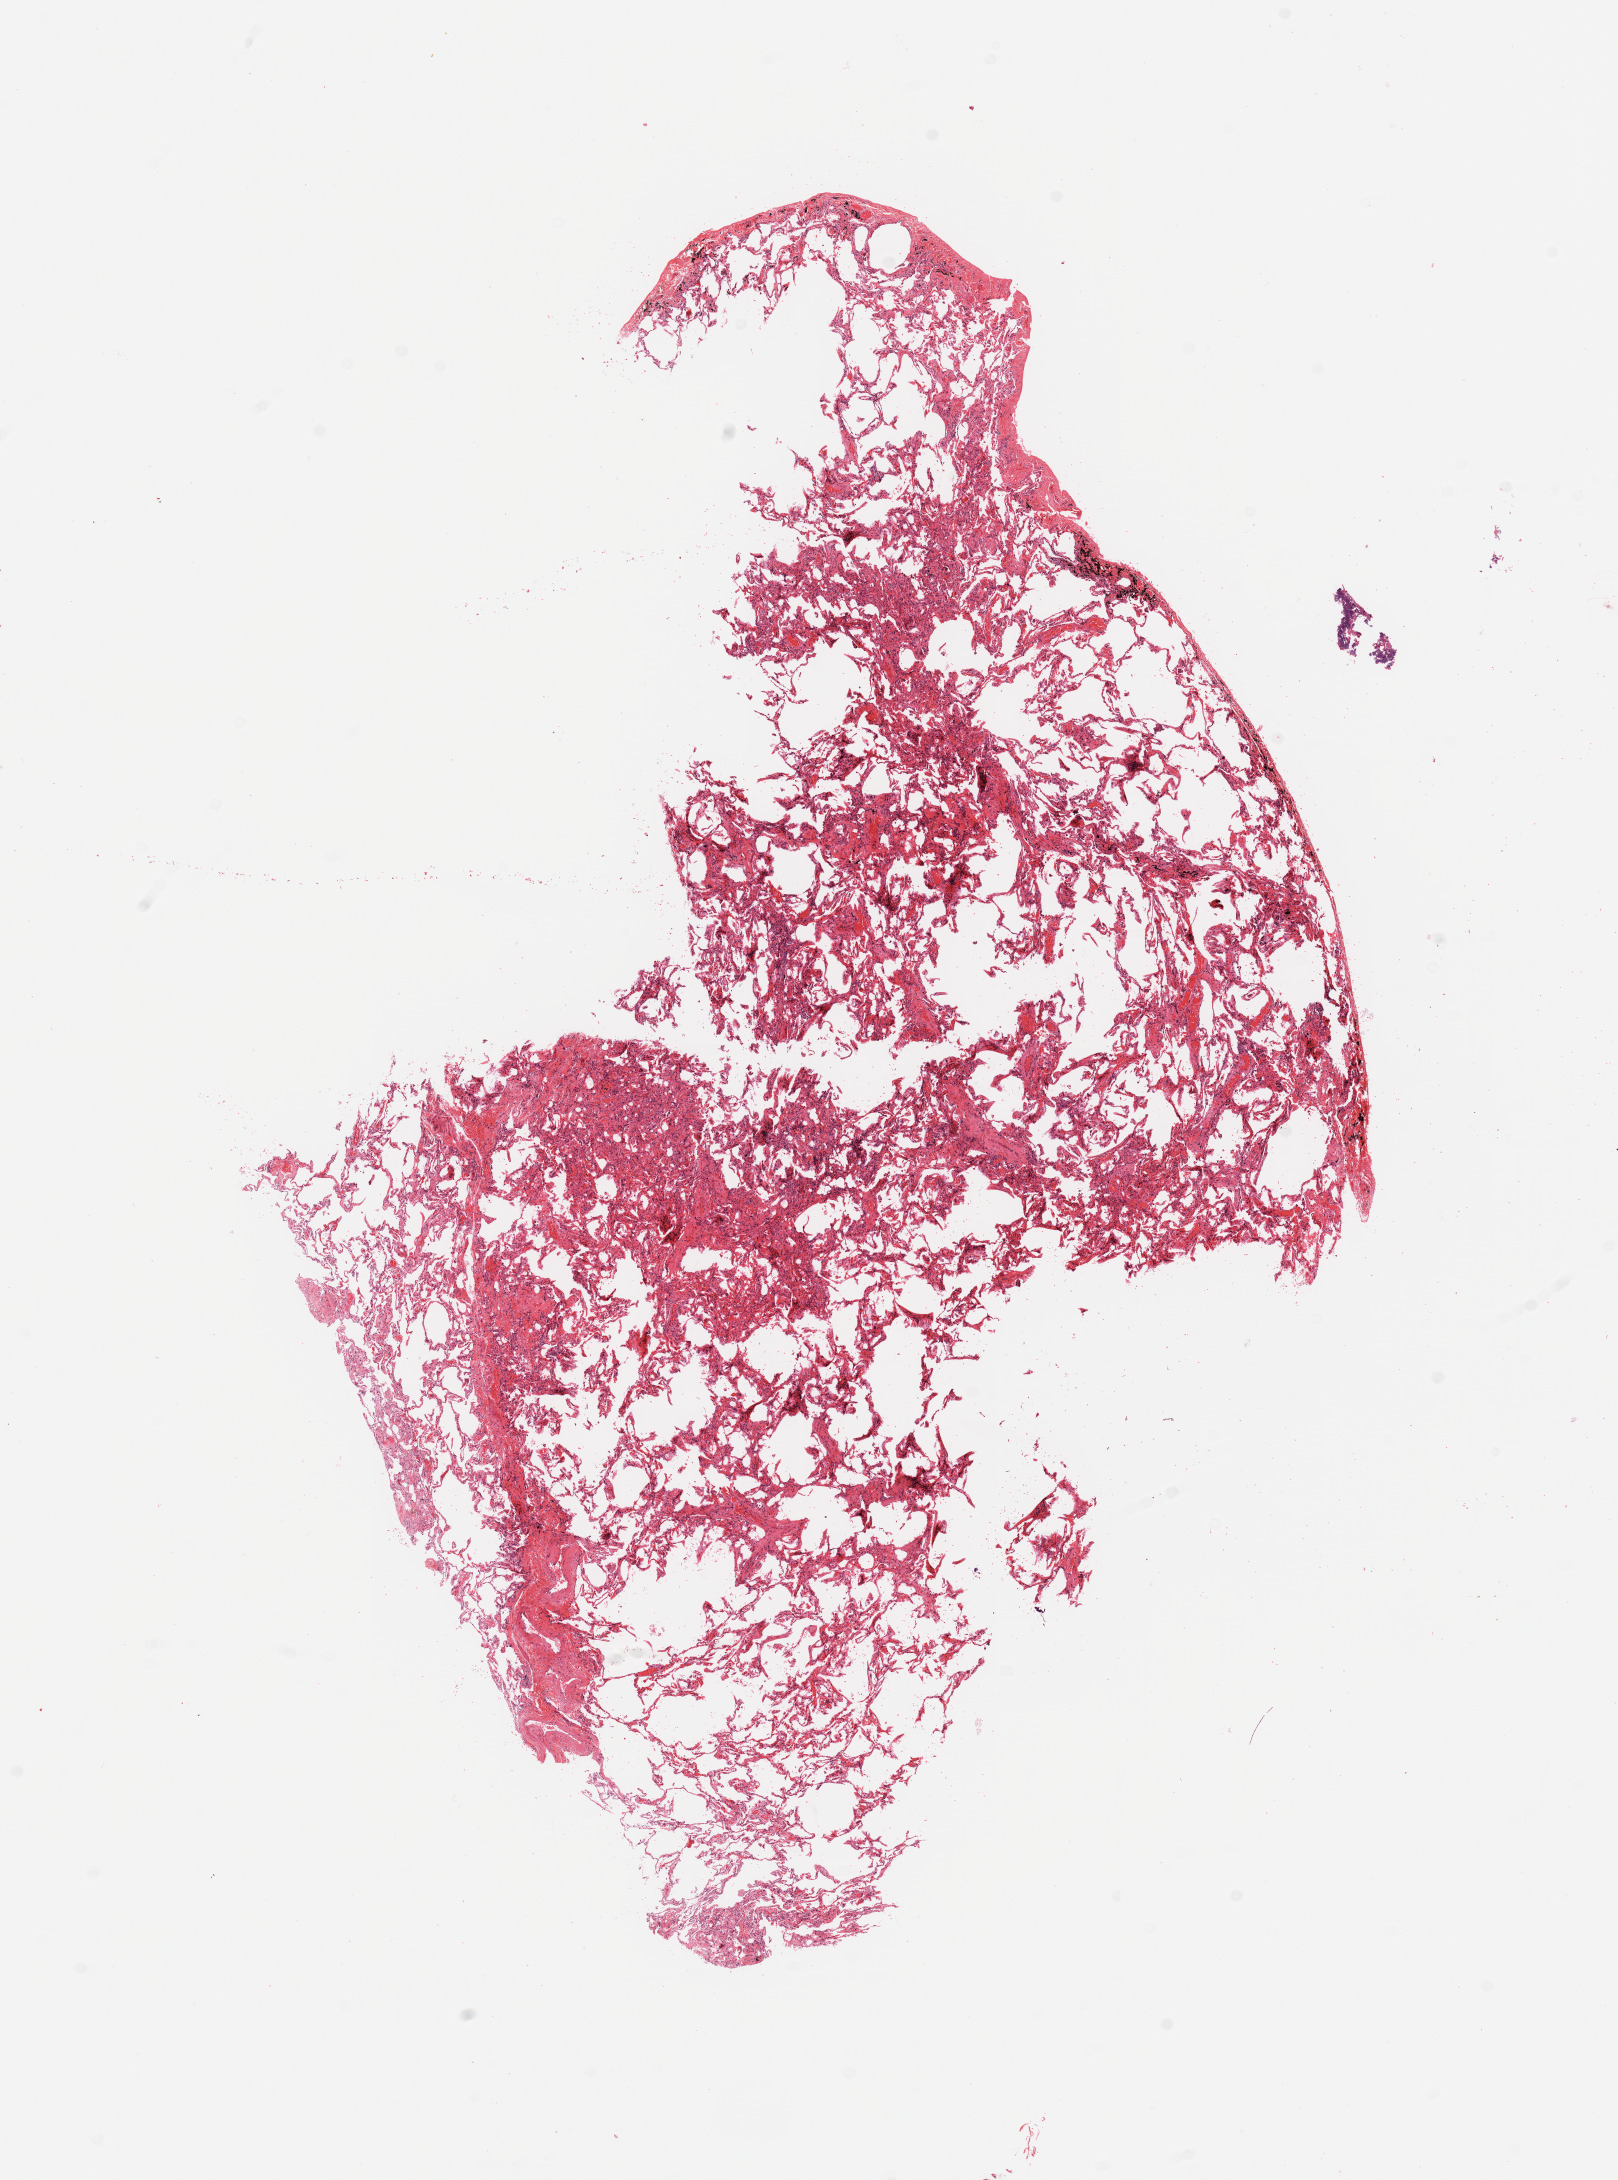
Whole-slide histology image, Hematoxylin and eosin (H&E) stained — whole scanned area (about 12.8 x 17.2 mm) shown as a low-resolution overview. Normal (non-tumour) tissue sample, sampled site: lung. 76-year-old male patient.
* this section: normal (non-tumour) tissue from the same patient
* patient diagnosis: Adenocarcinoma, NOS